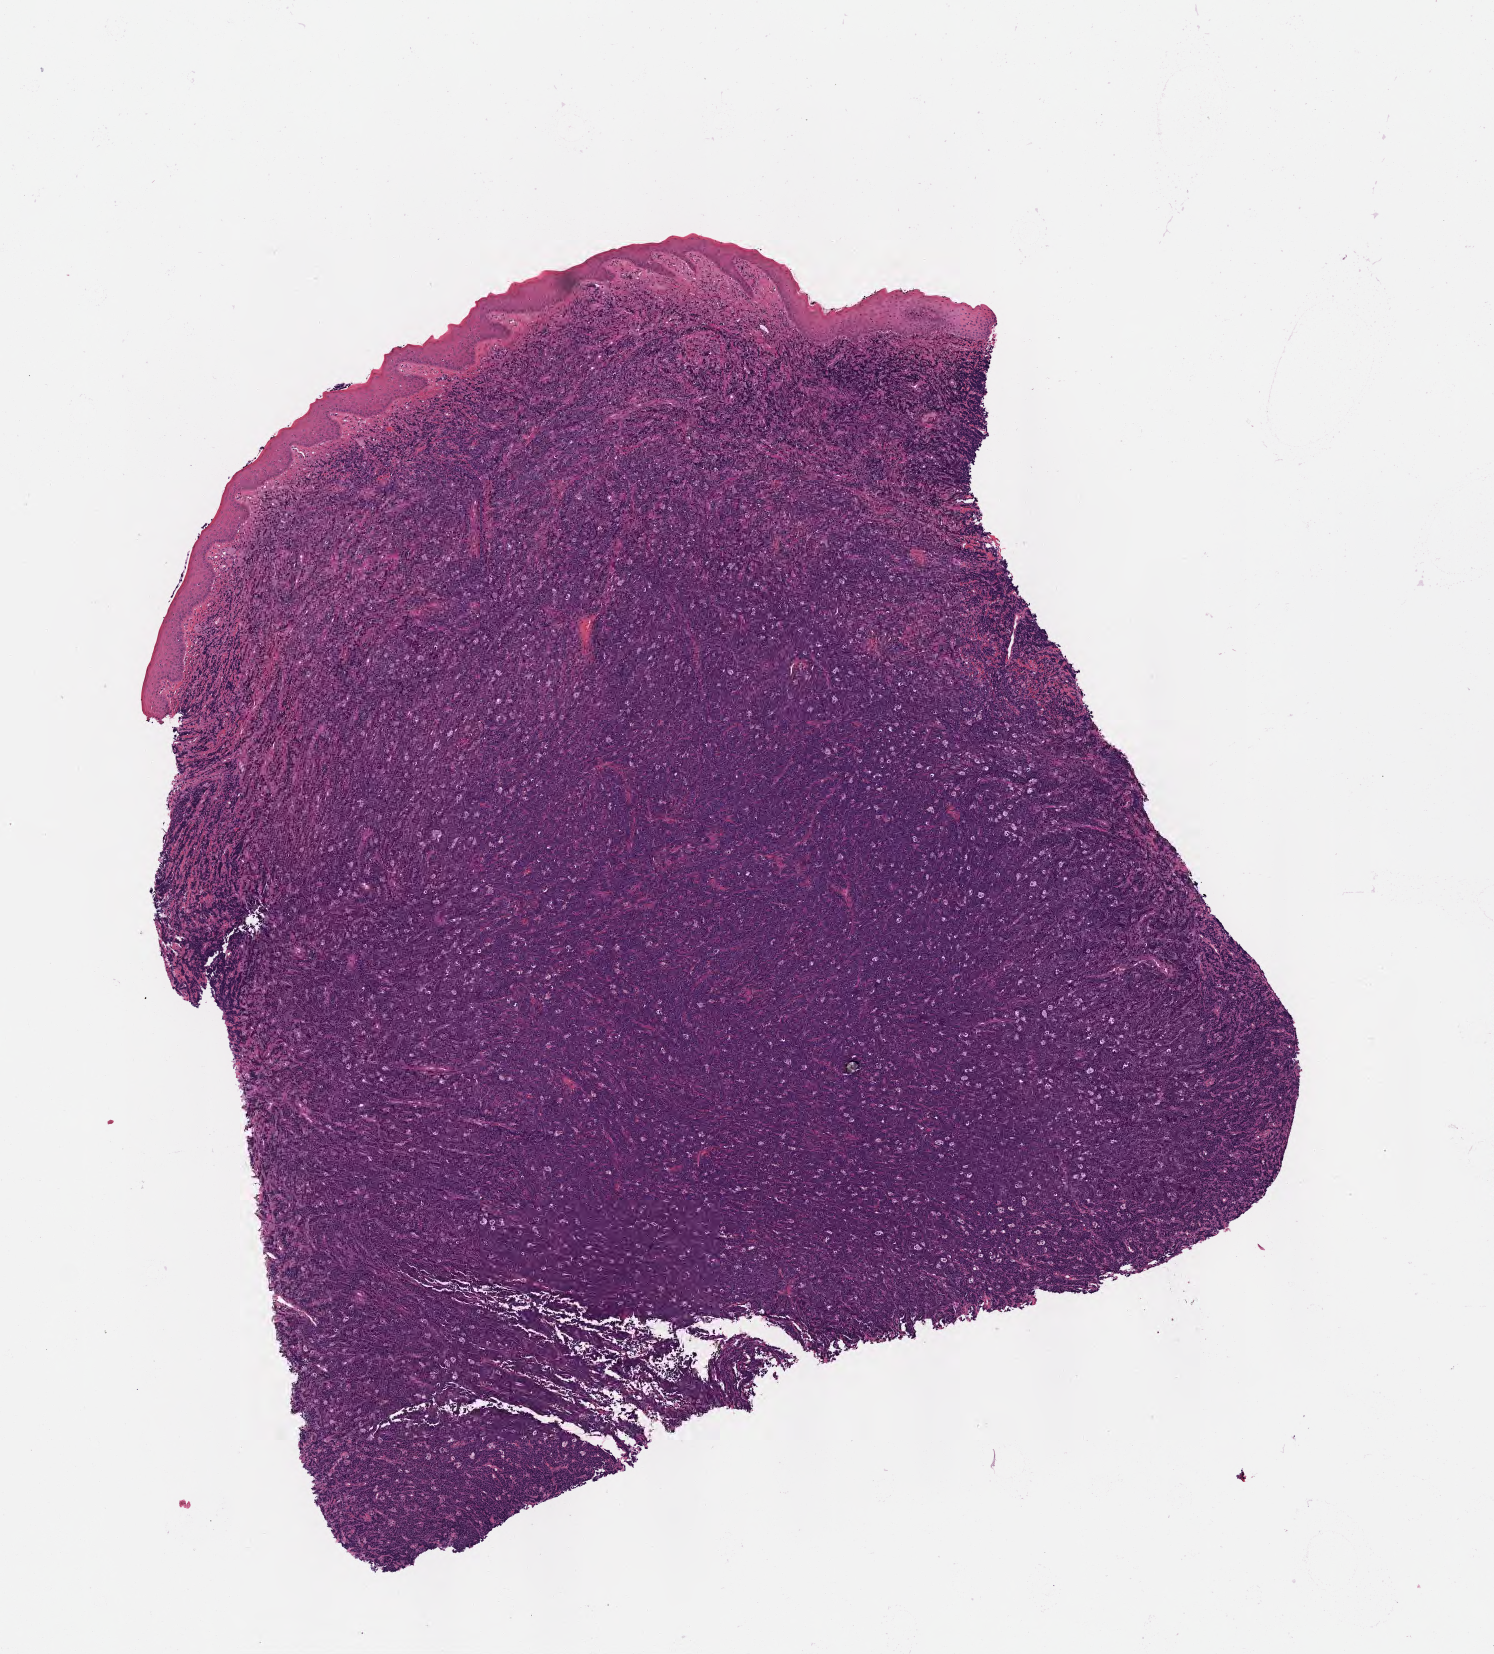
Haematoxylin and eosin whole-slide image — a low-resolution overview of the entire scanned area, about 6.0 x 6.7 mm; tumor tissue; site: mandible. Male patient; age at initial diagnosis 9 years.
- histologic diagnosis: Burkitt lymphoma, NOS